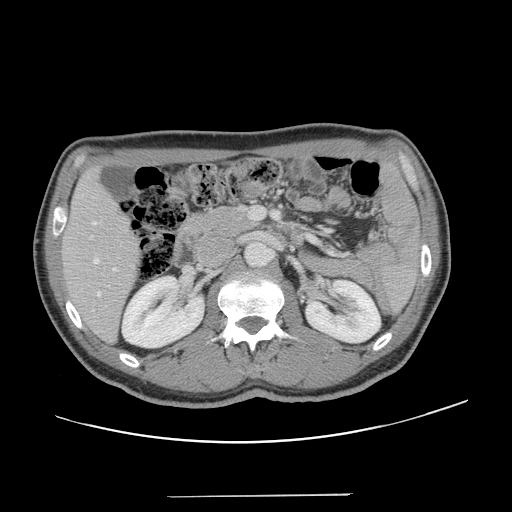
Contrast-enhanced abdominal CT, one axial slice; position 65 of 131 along the scan axis; 120 kVp; intravenous contrast given; soft-tissue window (W 400 / L 40 HU); 2.5 mm slice thickness; 512 × 512 image matrix, field of view 403 × 403 mm. Male patient, age 60 years. Case-level facts recorded for this patient, not image findings: diagnosis: colorectal cancer liver metastases, imaged before liver resection; multiple liver metastases: no; largest metastasis: 2.5 cm.
Annotated regions visible in this slice (expert manual segmentation):
- hepatic veins: box from (x=93, y=222) to (x=101, y=296) px
- liver: (x=63, y=172)–(x=139, y=341)
- planned liver remnant (the part of the liver to remain after resection): (x=63, y=172)–(x=139, y=341)